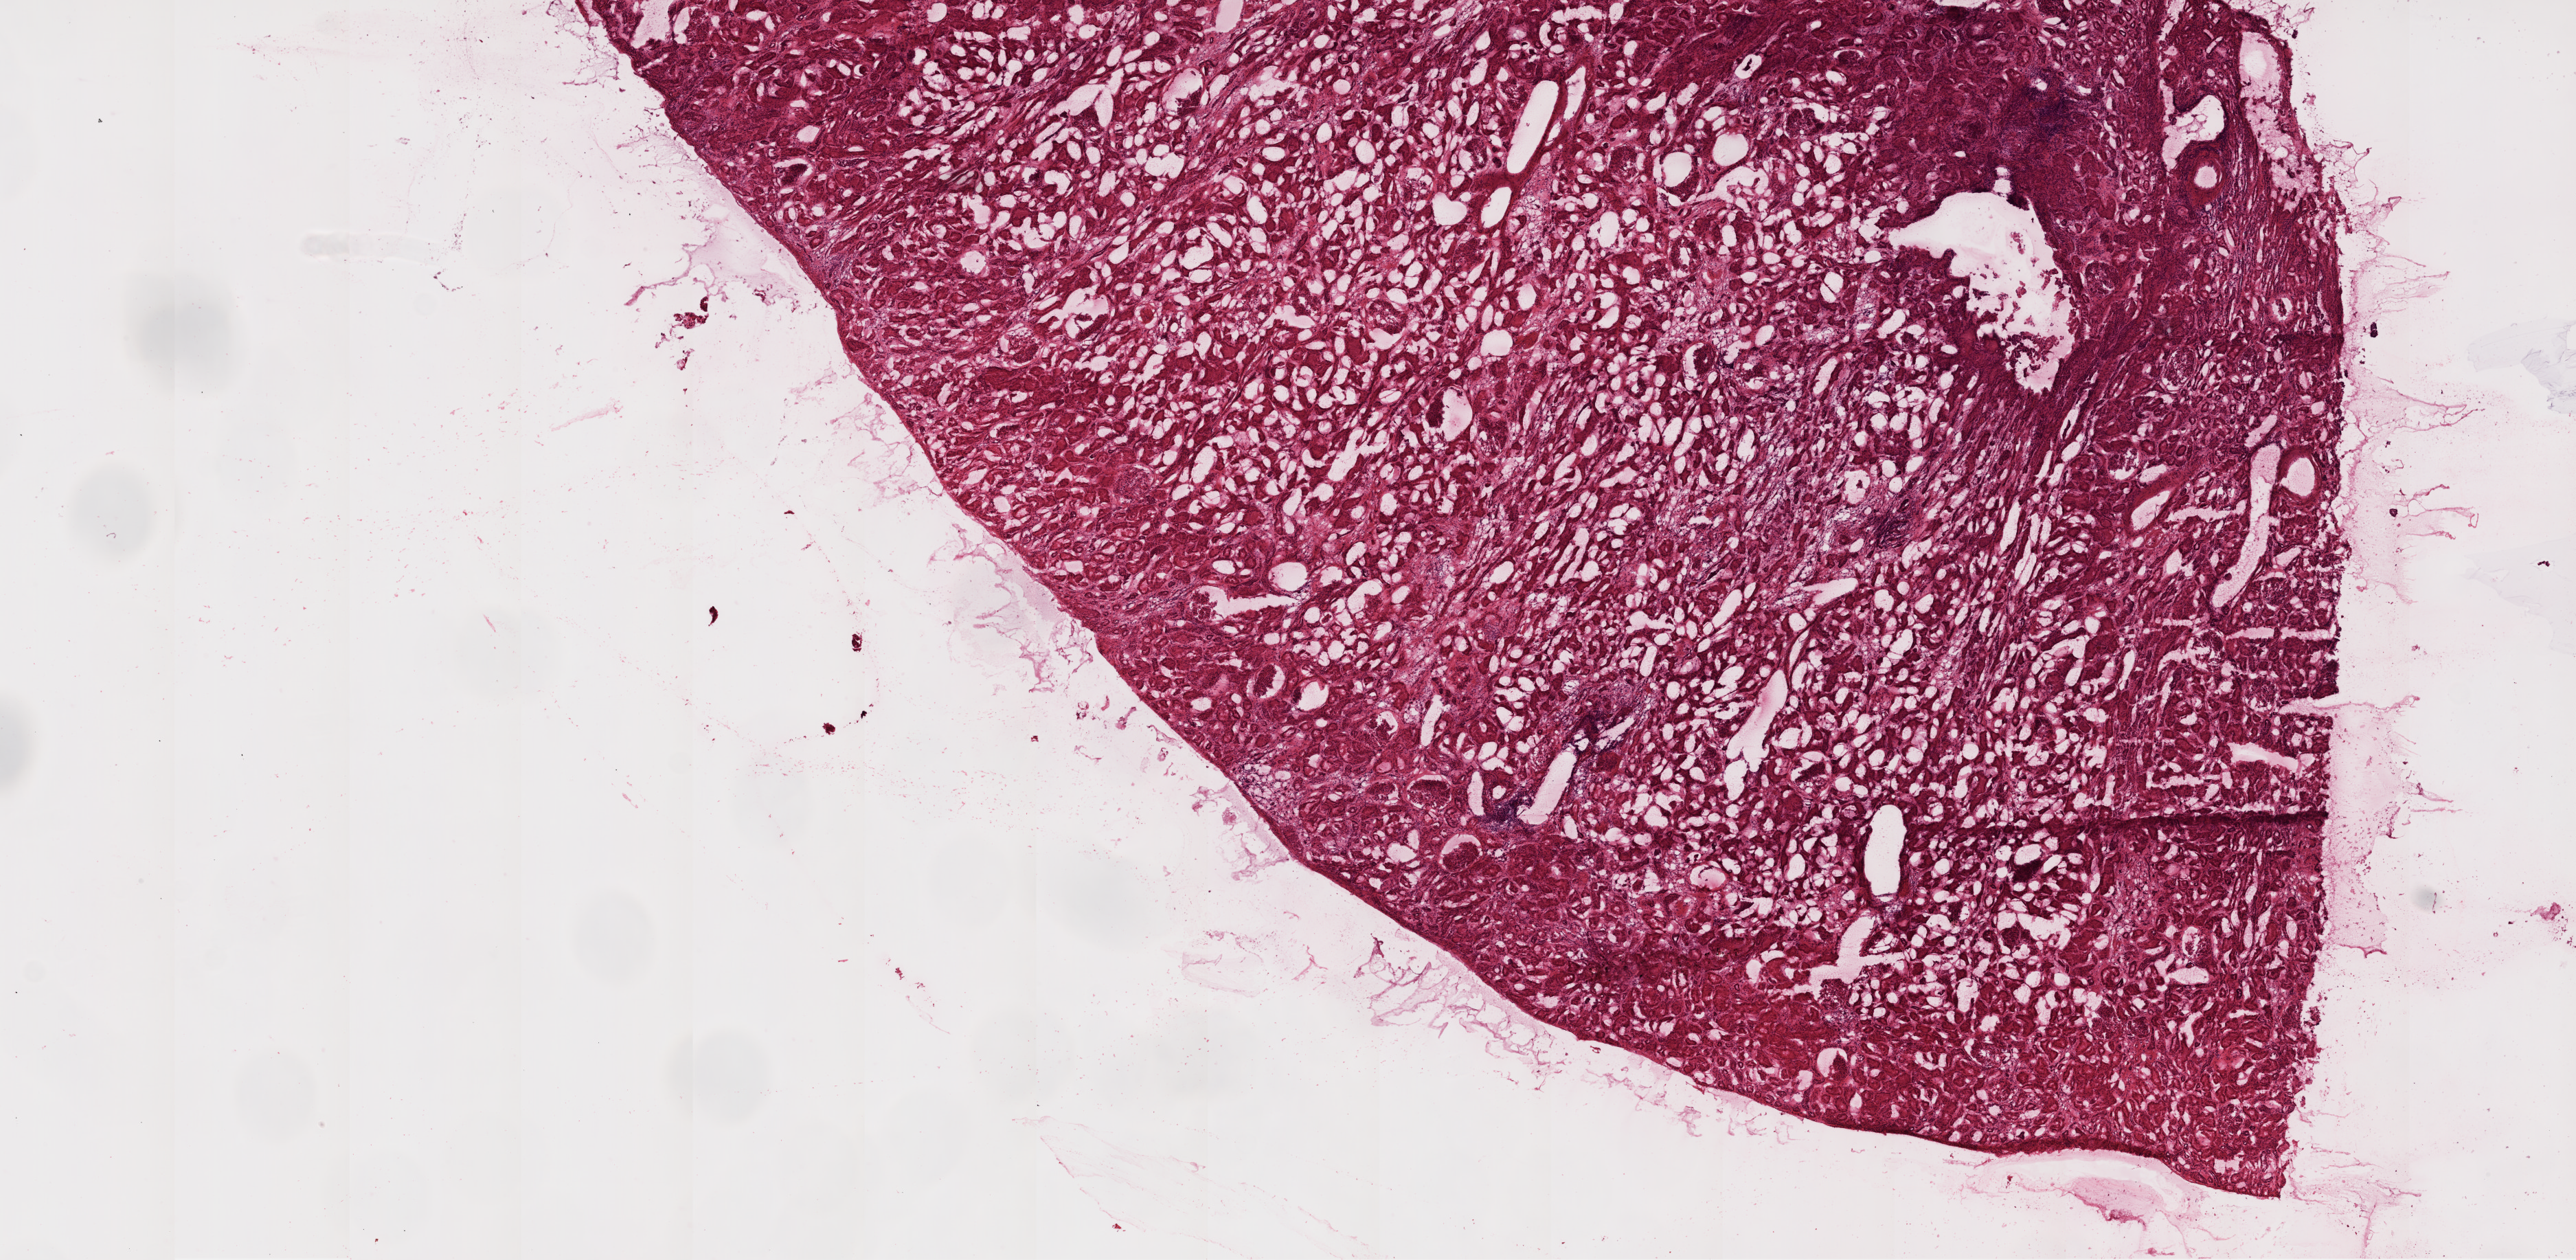
Digitized H&E-stained tissue section (whole slide) — a low-resolution overview of the entire scanned area, about 15.0 x 7.4 mm, frozen section from the top of the tissue portion, kidney, solid tissue normal (non-tumour tissue) sample. Female patient; age at initial diagnosis 60 years.
This section: solid tissue normal (non-tumour) sample from the same patient. Patient diagnosis: Clear cell adenocarcinoma, NOS.